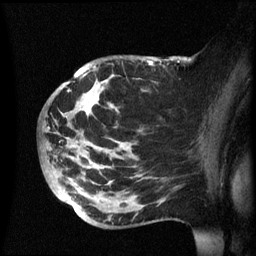
Breast MRI (dynamic contrast-enhanced), one sagittal slice. Position 37 of 60 along the scan axis. Dynamic contrast-enhanced series, image 2 of 3 at this slice position (ordered by acquisition). 1.5 T. TE 4.2 ms, TR 8.4 ms. 2.4 mm slice thickness. 256 × 256 image matrix, field of view 230 × 230 mm. Patient: female, 49 years.
Outlined on this slice (semi-automatic segmentation, software-assisted and operator-edited):
- analysis volume of interest (the breast-tissue region the enhancement analysis was run in; not a lesion): bounding box <42,56,174,228> (left, top, right, bottom; pixels)
- tumour enhancement mask (voxels above the 70 % enhancement threshold inside the analysis volume of interest): <70,74,129,184>